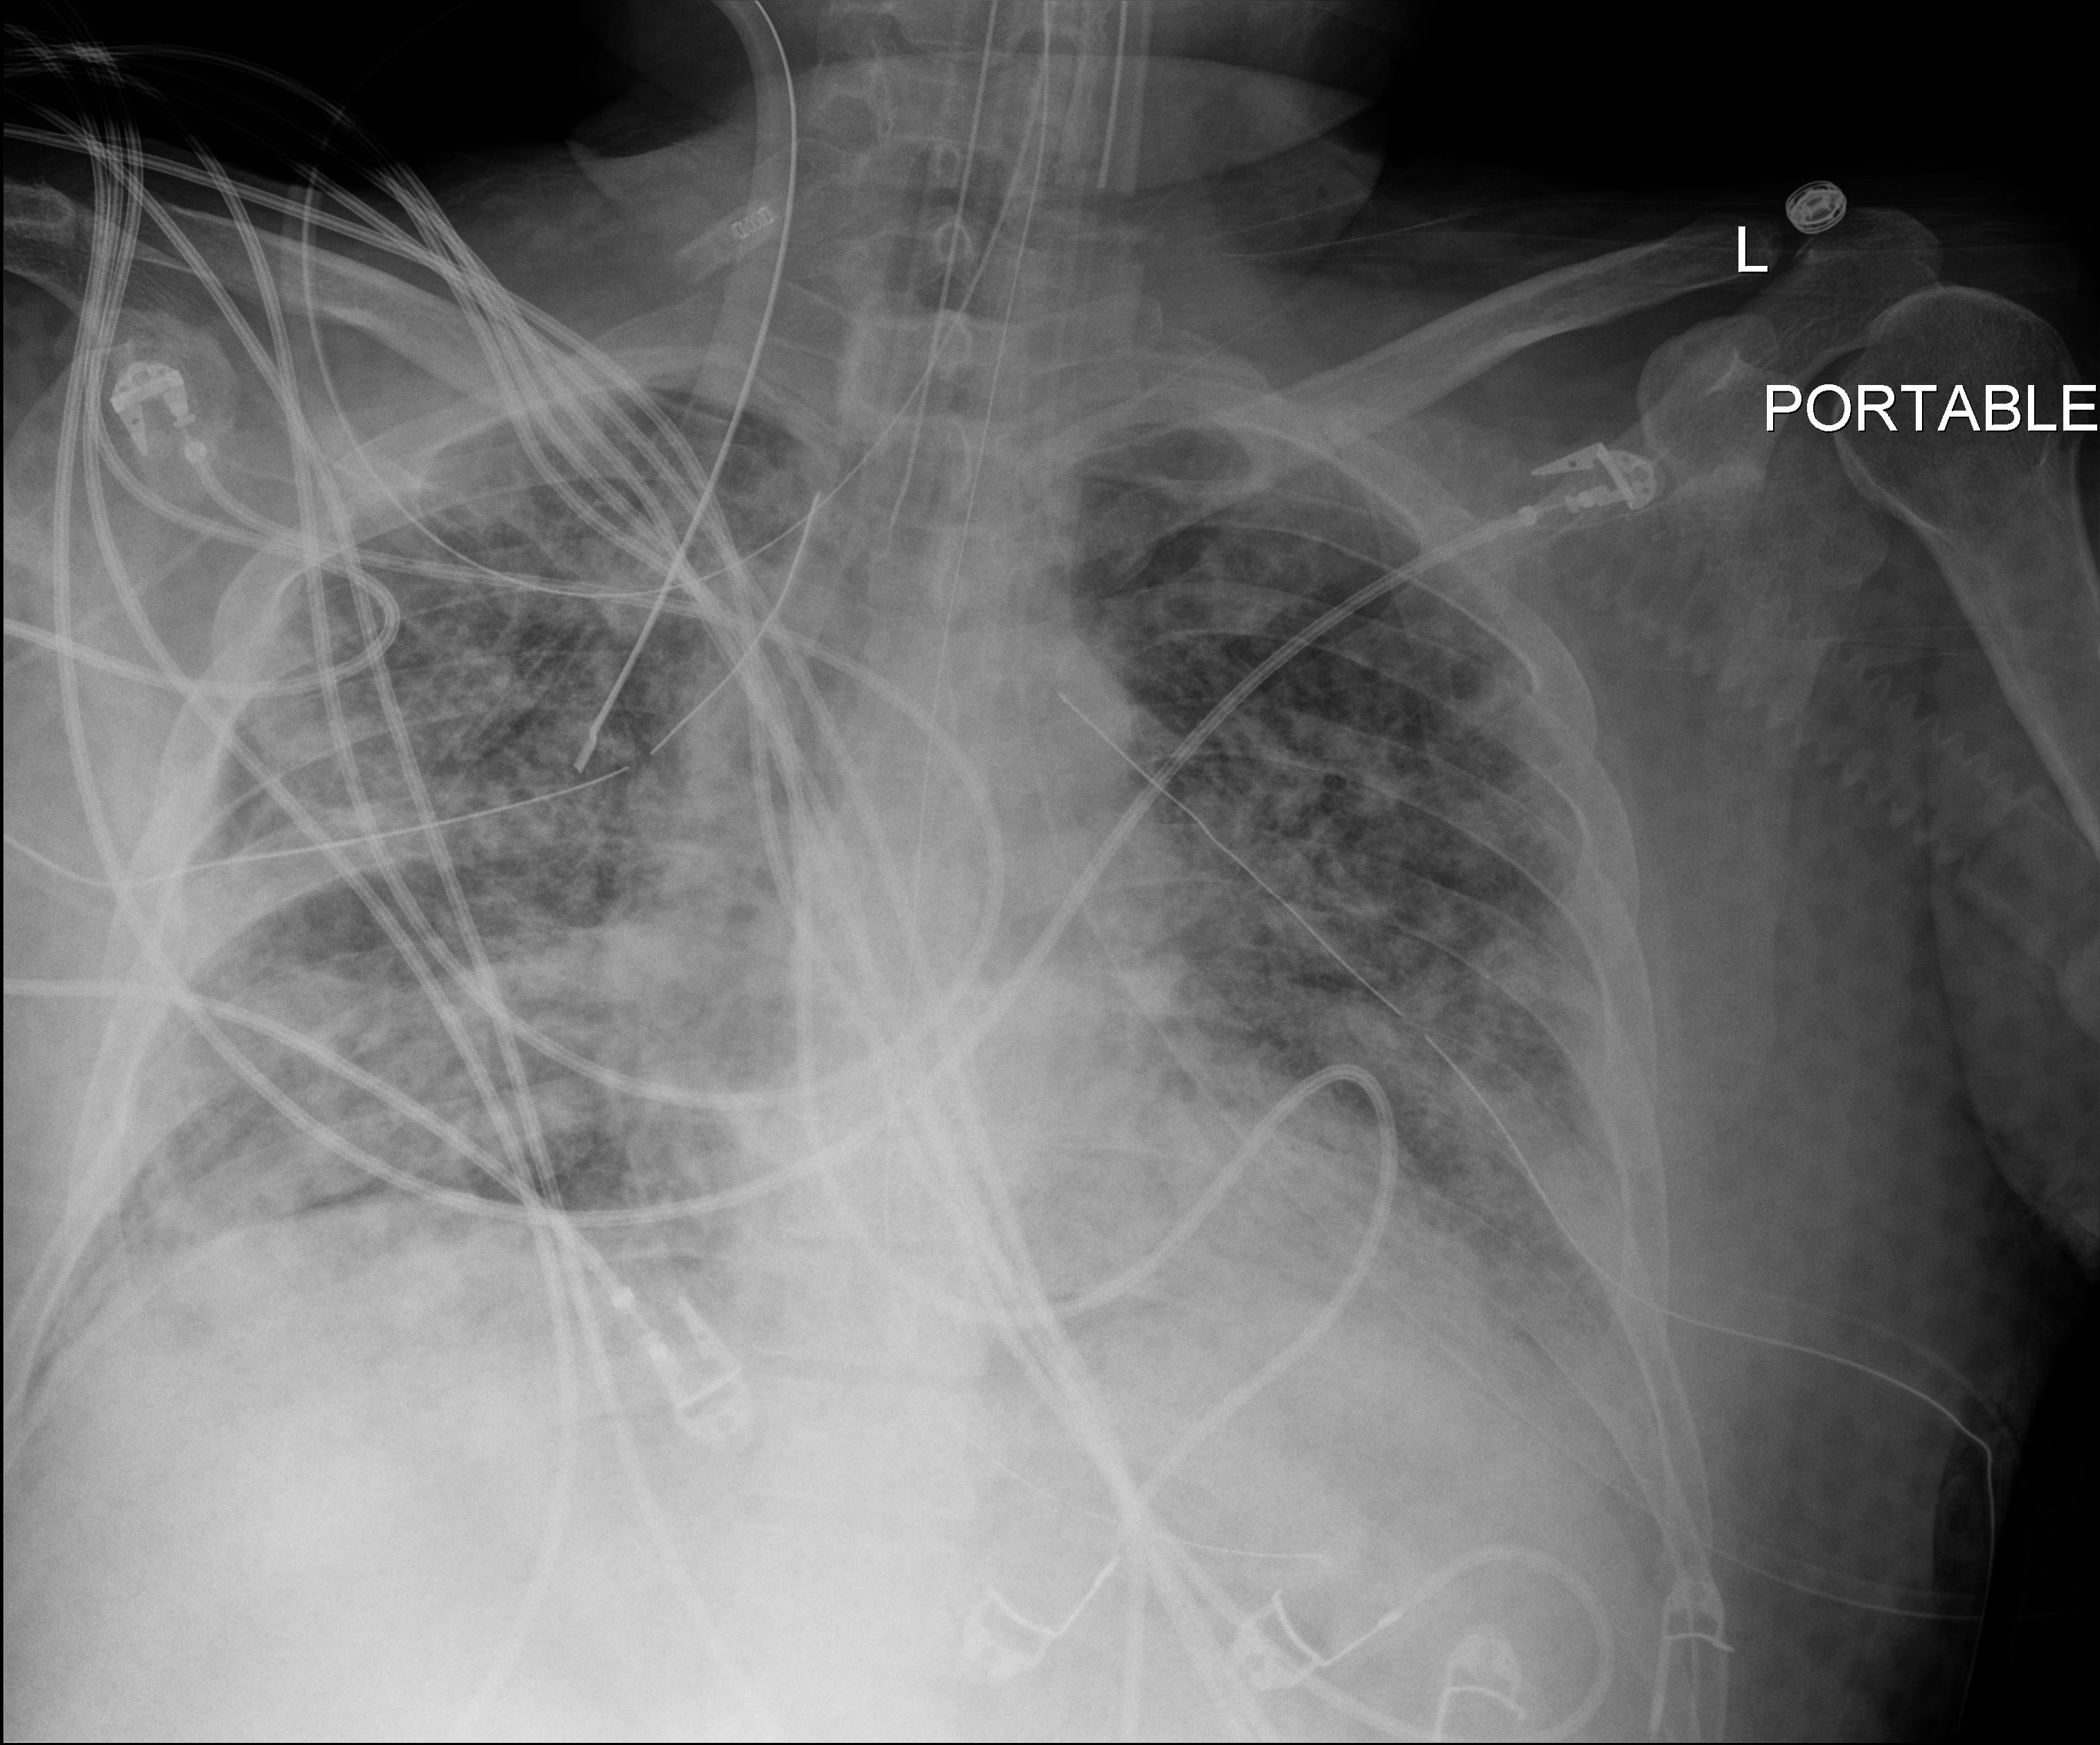
Chest X-ray (portable), anteroposterior (AP) projection. Male patient hospitalised with COVID-19, age 18–59 years.
Hospital-stay facts (about this admission, not read from this image; timing relative to this image not recorded): mechanically ventilated during this hospital stay: yes; length of hospital stay: 63 days.